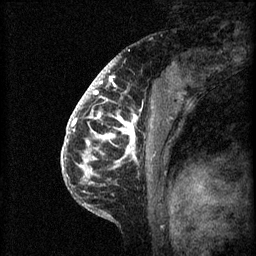
Breast MRI (dynamic contrast-enhanced), one sagittal slice. Slice 42 of 60 in the series (ordered by position). 3 images stored at this slice position (order not interpretable as contrast timing). 1.5 T. TE 4.2 ms, TR 8.2 ms. 256 × 256 image matrix, field of view 180 × 180 mm. Female patient, age 41 years.
Annotated regions visible in this slice (semi-automatic segmentation, software-assisted and operator-edited):
- analysis volume of interest (the breast-tissue region the enhancement analysis was run in; not a lesion): bounding box [x1, y1, x2, y2] px = [72, 108, 159, 201]
- tumour enhancement mask (voxels above the 70 % enhancement threshold inside the analysis volume of interest): [72, 108, 139, 175]